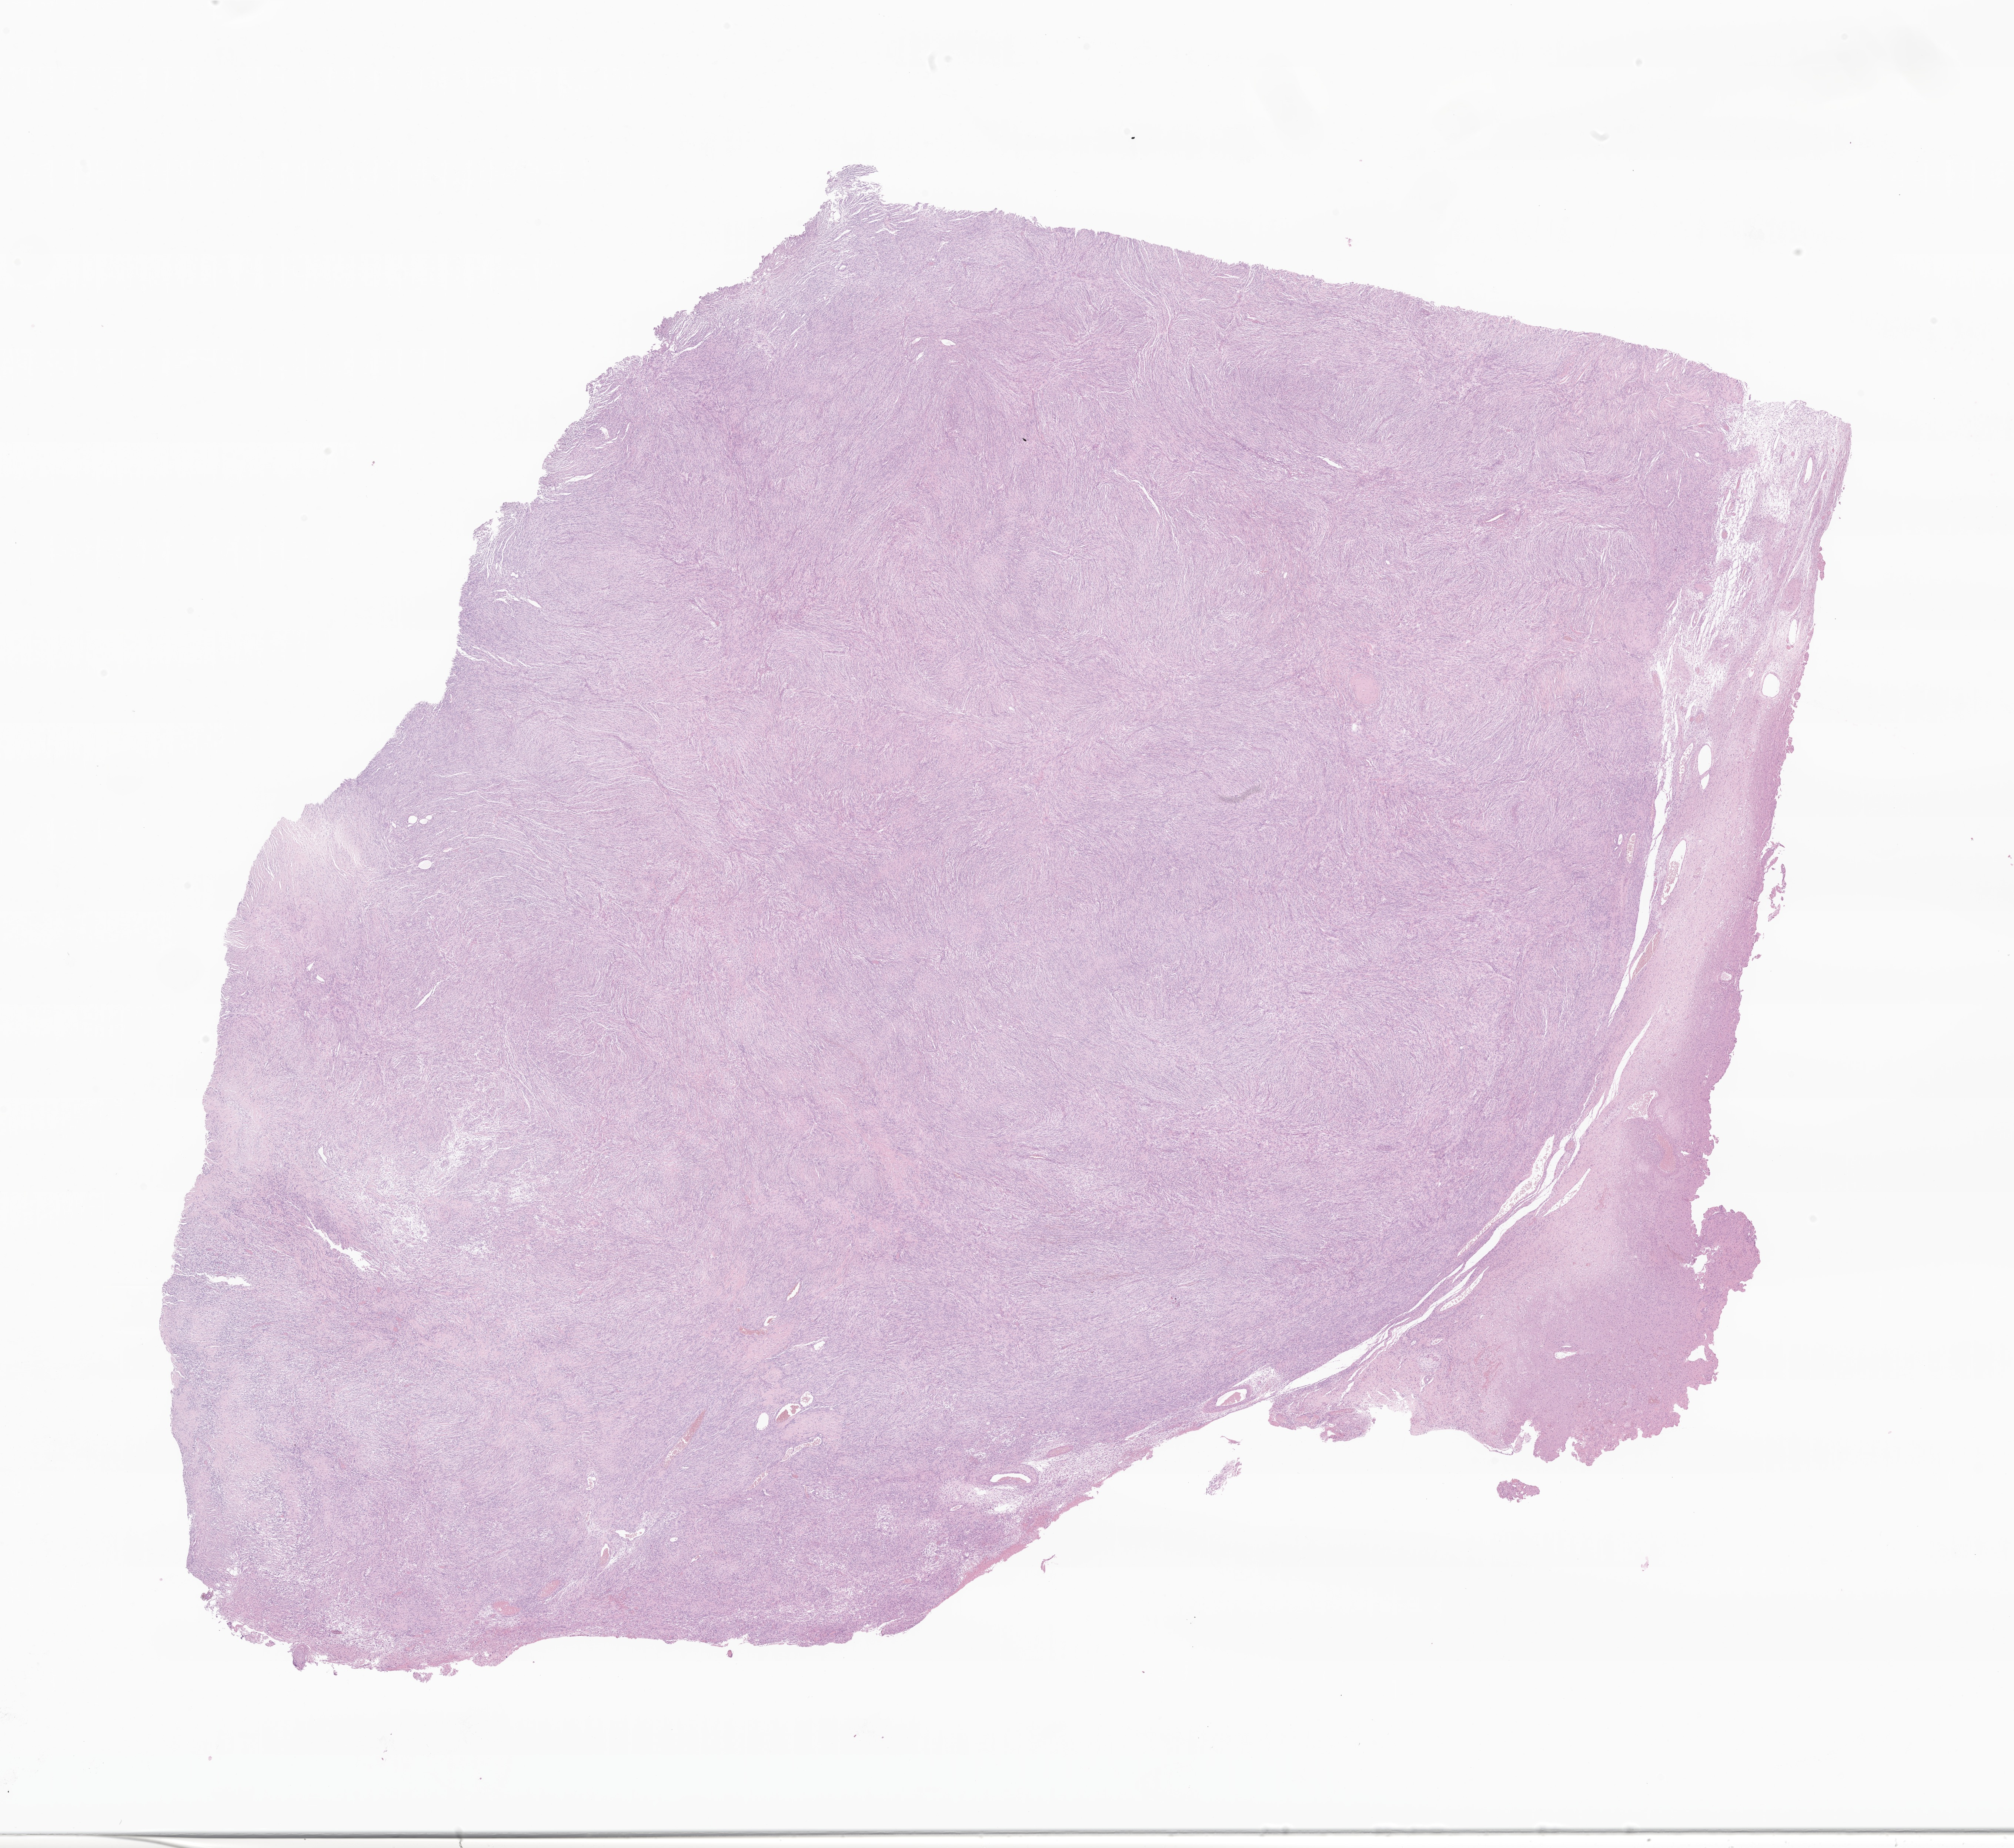
Whole-slide image, hematoxylin and eosin (H&E) stain of tumor tissue from the cerebrum — a low-resolution overview of the entire scanned area, about 22.9 x 21.0 mm; formalin-fixed, paraffin-embedded (FFPE) tissue. Patient male; age 61 months (5 years 1 month).
Diagnosis (ICD-O-3 morphology term): Meningioma, NOS.